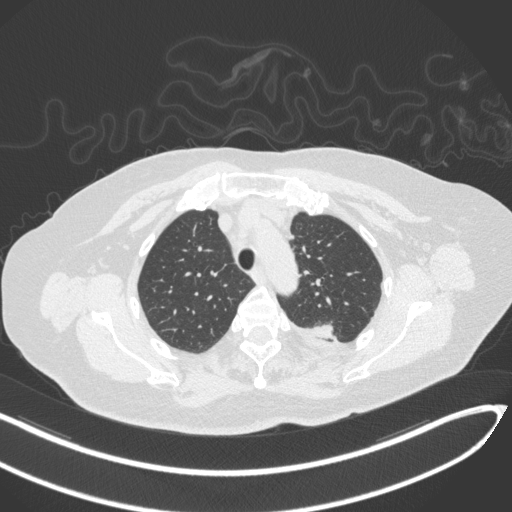
Chest CT, one axial slice. Position 253 of 270 along the scan axis. Reconstruction kernel B31f. Lung window (W 1500 / L -600 HU). 1 mm slice thickness. 512 × 512 image matrix. Female patient, age 76 years. From the clinical record (not read from this slice): clinical TNM (as recorded): T1c N0 M0.
Outlined on this slice (rectangle marked by the reading radiologist):
- lung tumour (recorded histology: adenocarcinoma): box from (x=305, y=319) to (x=336, y=343) px